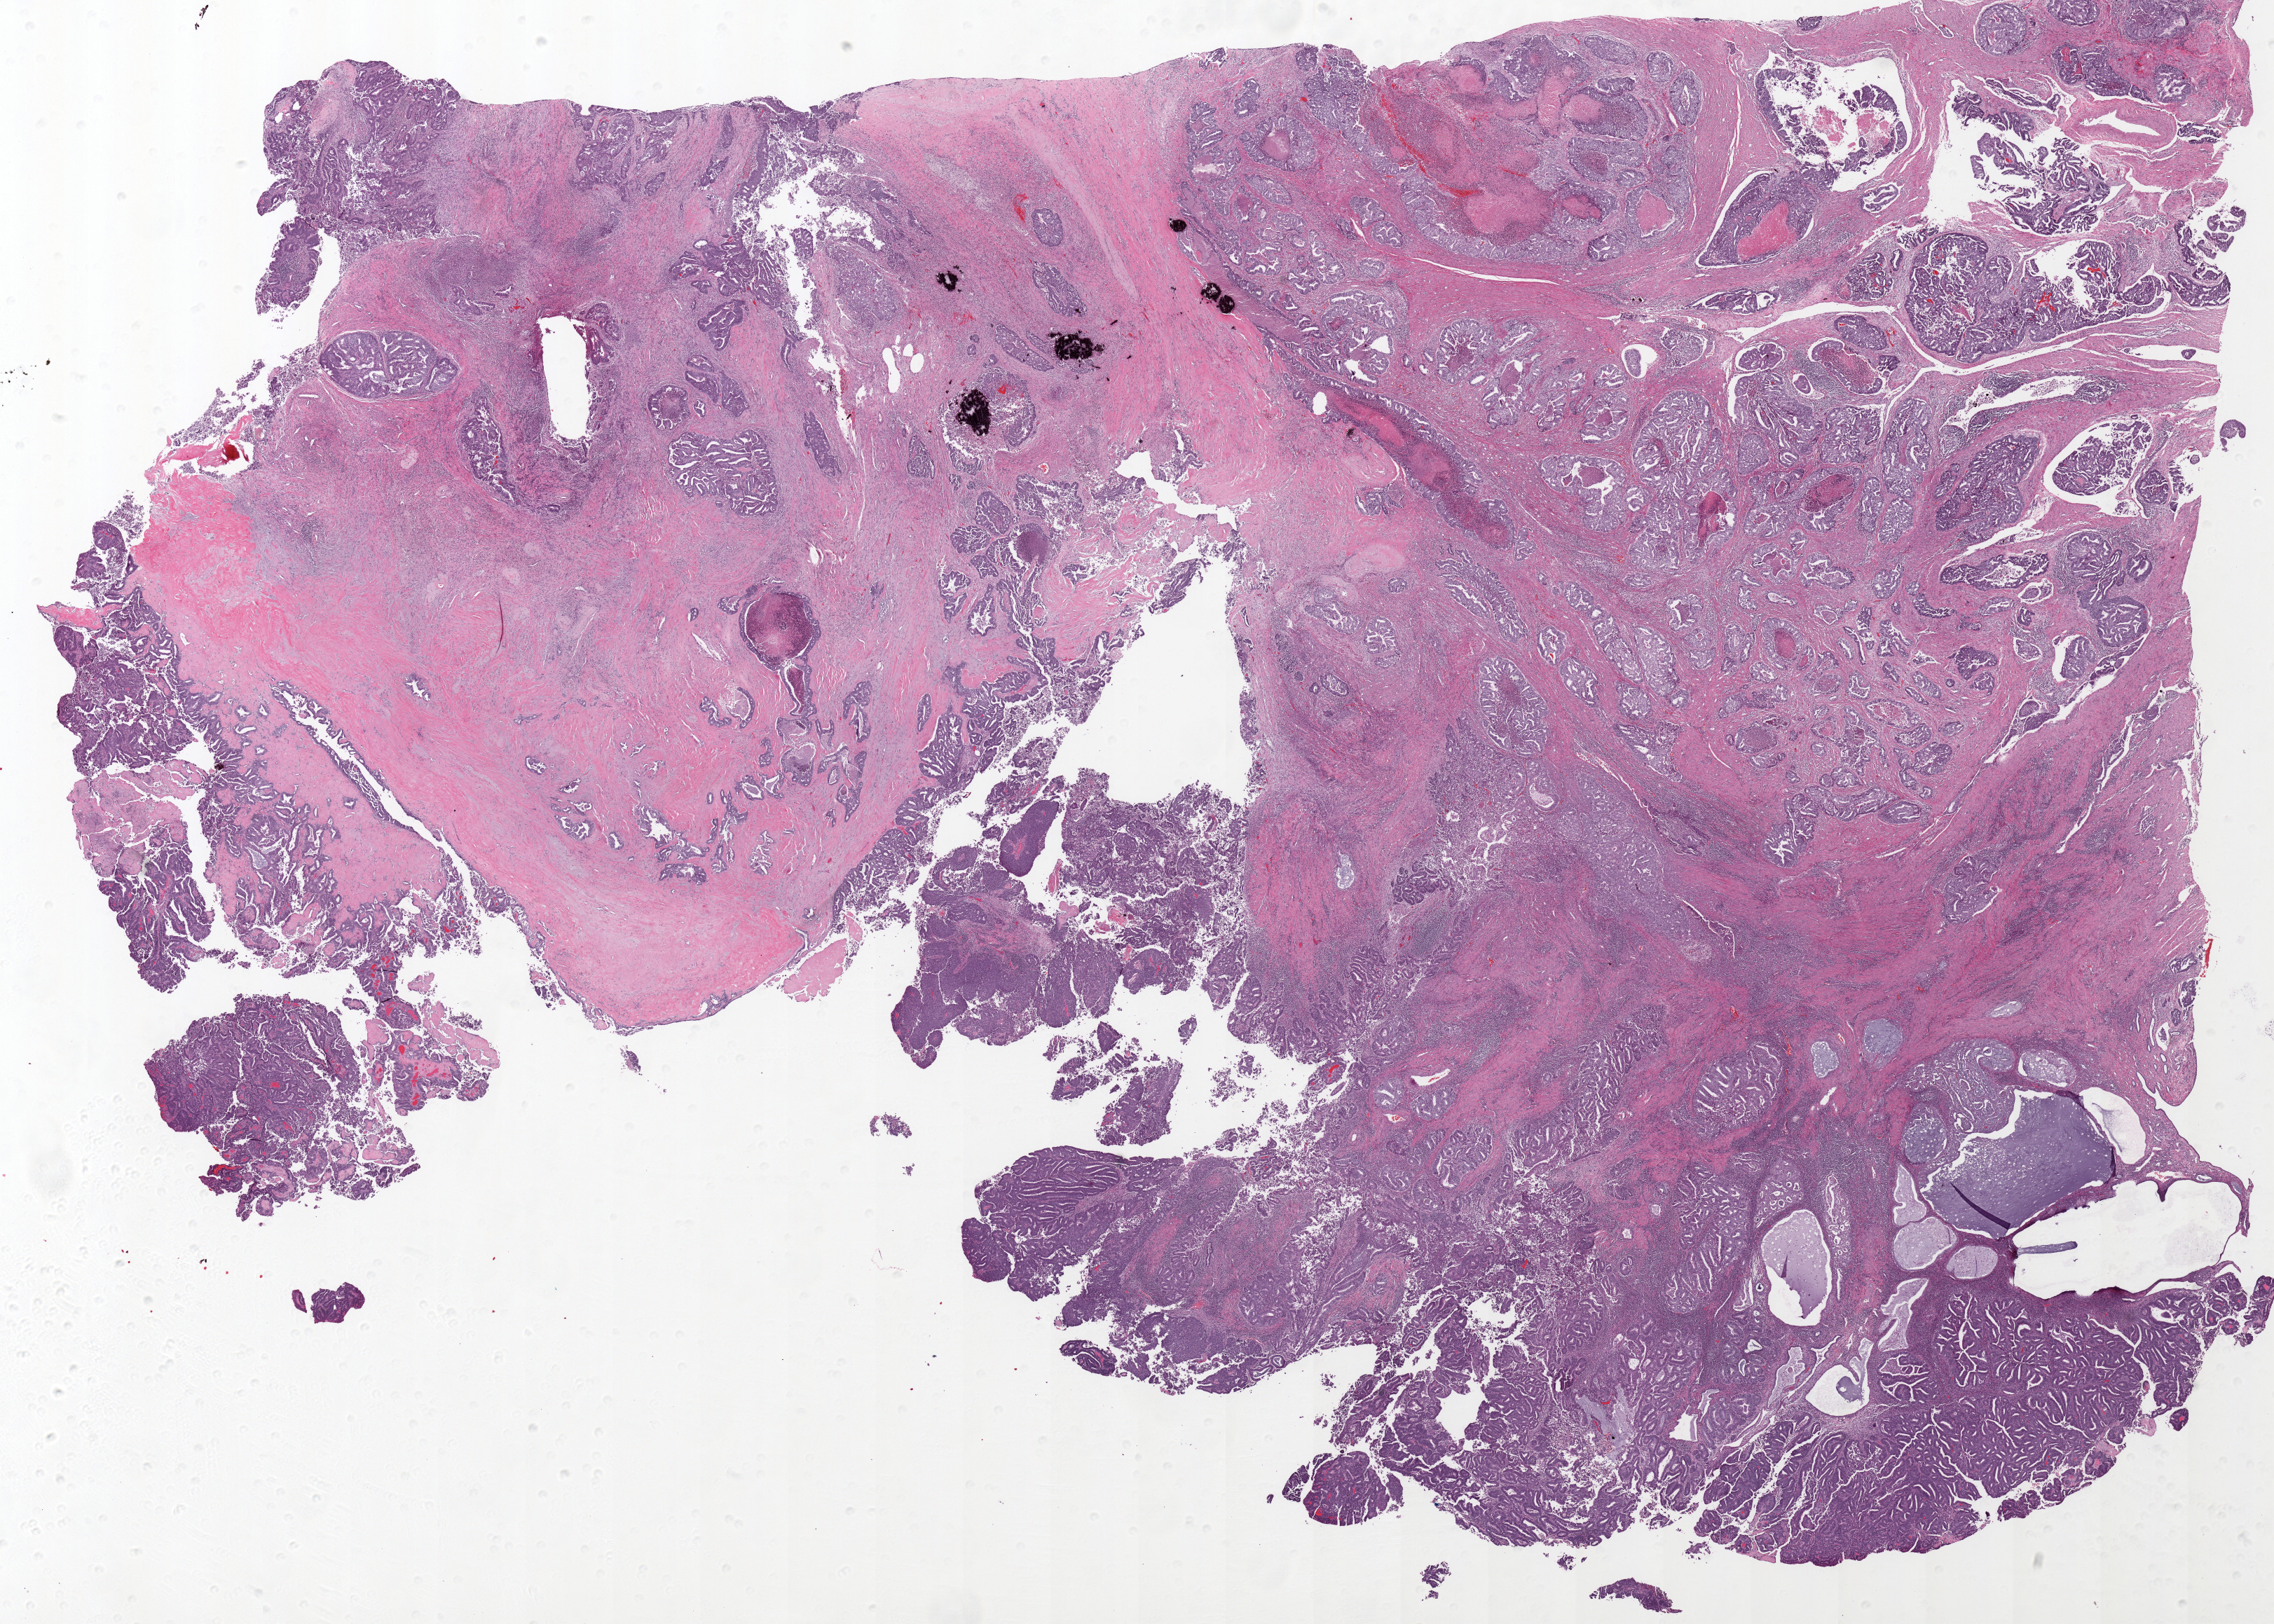
H&E whole-slide image, shown as a low-resolution overview of the whole scanned area (about 25.9 x 18.5 mm). FFPE section. Sample: primary tumour, uterus. Female patient; age at initial diagnosis 68 years.
Histologic diagnosis: Endometrioid adenocarcinoma, NOS (endometrium).